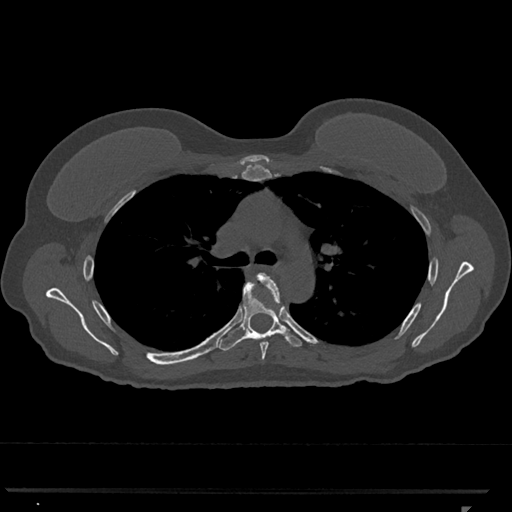
CT including the spine, one axial slice; position 780 of 793 along the scan axis; reconstruction kernel Br40s/3; 120 kVp; bone window (W 1800 / L 400 HU); 0.5 mm slice thickness; 512 × 512 image matrix, field of view 380 × 380 mm. Patient: female, 62 years. From the clinical record (not read from this slice): primary cancer: renal.
Outlined on this slice (semi-automatic segmentation, software-assisted and operator-edited):
- T5 vertebra: bounding box [x1, y1, x2, y2] px = [258, 272, 285, 360]
- T6 vertebra: [219, 279, 302, 351]